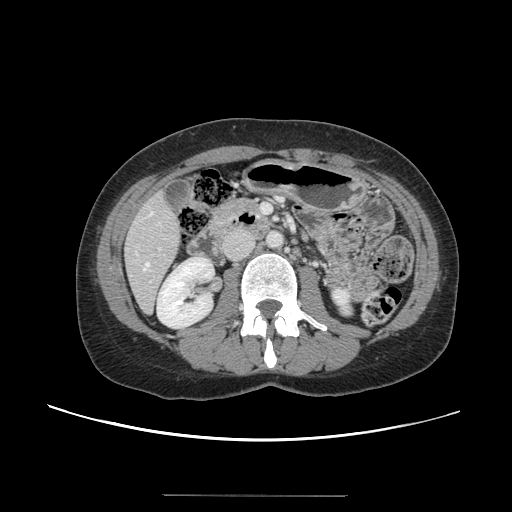
Contrast-enhanced abdominal CT, one axial slice; position 46 of 144 along the scan axis; intravenous contrast given; soft-tissue window (W 400 / L 40 HU); 2.5 mm slice thickness; 512 × 512 image matrix, field of view 380 × 380 mm. Female patient, age 53 years. From the clinical record (not read from this slice): diagnosis: colorectal cancer liver metastases, imaged before liver resection; multiple liver metastases: yes; largest metastasis: 1.1 cm; disease in both lobes: no.
Structures marked on this image (outlined manually by an expert reader):
- hepatic veins: bounding box <144,263,149,270> (left, top, right, bottom; pixels)
- liver: <125,194,181,312>
- planned liver remnant (the part of the liver to remain after resection): <126,194,182,312>
- portal vein (with intrahepatic branches): <149,248,161,283>